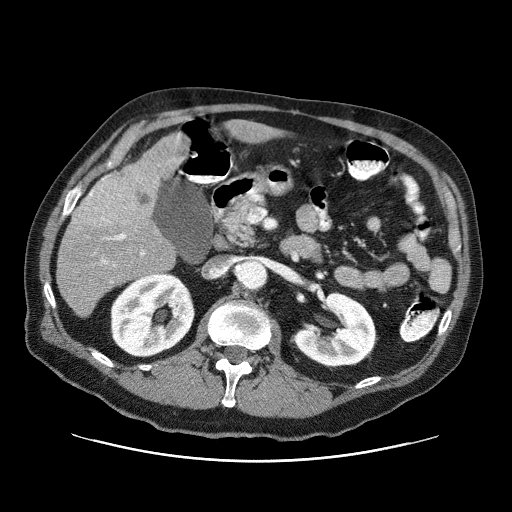
Contrast-enhanced abdominal CT (liver protocol), one axial slice; position 28 of 87 along the scan axis; reconstruction kernel STANDARD; one of 3 acquisitions stored at this slice position; soft-tissue window (W 400 / L 40 HU); 2.5 mm slice thickness; 512 × 512 image matrix, field of view 400 × 400 mm. From the clinical record (not read from this slice): diagnosis: hepatocellular carcinoma (patient treated with transarterial chemoembolisation; whether this scan precedes or follows treatment is not stated here); TNM stage (as recorded): Stage-IIIA; Child-Pugh class: A; tumour differentiation: well differentiated; tumour nodularity: multinodular.
Outlined on this slice (semi-automatically segmented with operator editing):
- liver parenchyma outside the tumour (the mass and vessels are separate outlines, so this box may not span the whole liver): bounding box [x1, y1, x2, y2] px = [56, 120, 244, 318]
- mass: [69, 156, 164, 236]
- liver vessels: [90, 135, 180, 266]